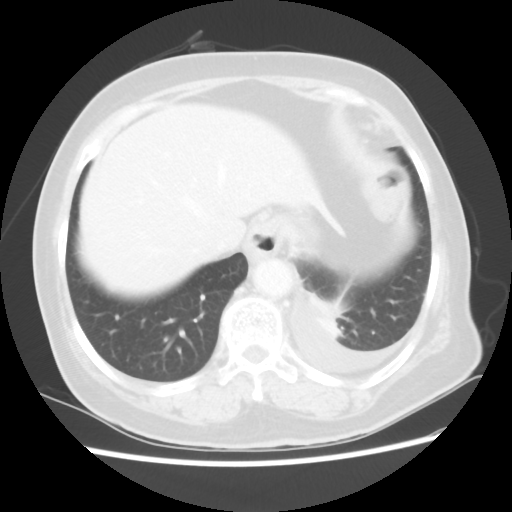
Chest CT, one axial slice. Slice 6 of 80 in the series (ordered by position). 100 kVp. Lung window (W 1500 / L -600 HU). 5 mm slice thickness. 512 × 512 image matrix. Female patient, age 68 years. Case-level facts recorded for this patient, not image findings: clinical TNM (as recorded): T1c N0 M1.
Annotated regions visible in this slice (bounding box drawn by a radiologist):
- lung tumour (recorded histology: adenocarcinoma): bounding box <308,288,348,340> (left, top, right, bottom; pixels)